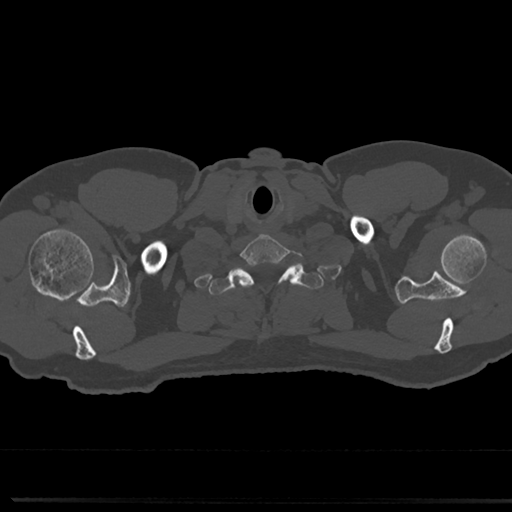
CT including the spine, one axial slice. Position 689 of 817 along the scan axis. Bone window (W 1800 / L 400 HU). 512 × 512 image matrix, field of view 355 × 355 mm. Male patient, age 61 years. Case-level facts recorded for this patient, not image findings: primary cancer: prostate.
Annotated regions visible in this slice (semi-automatic segmentation, software-assisted and operator-edited):
- T1 vertebra: bounding box <211,262,318,344> (left, top, right, bottom; pixels)